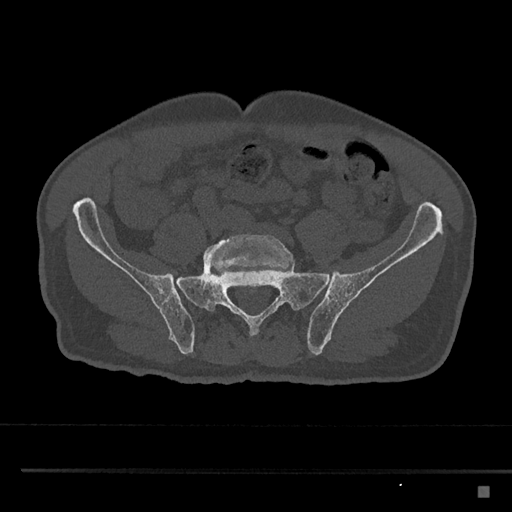
CT including the spine, one axial slice. Slice 549 of 797 in the series (ordered by position). Reconstruction kernel Br40s/3. Bone window (W 1800 / L 400 HU). 512 × 512 image matrix, field of view 391 × 391 mm. Patient: male, 59 years. From the clinical record (not read from this slice): primary cancer: prostate.
Structures marked on this image (semi-automatically segmented with operator editing):
- L5 vertebra: bounding box [x1, y1, x2, y2] px = [203, 234, 292, 275]